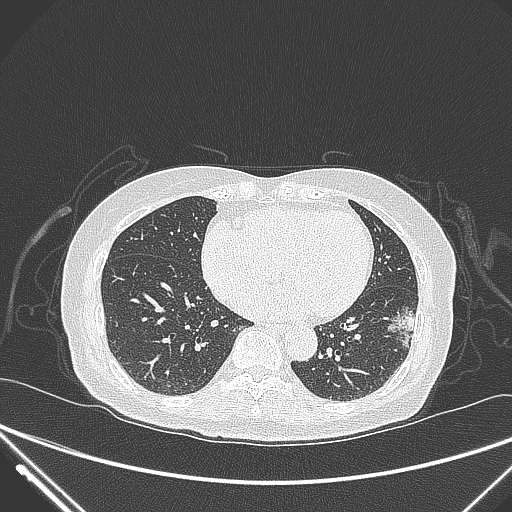
Chest CT, one axial slice; position 113 of 310 along the scan axis; lung window (W 1500 / L -600 HU); 1 mm slice thickness; 512 × 512 image matrix, field of view 377 × 377 mm. Female patient, age 82 years. Case-level facts recorded for this patient, not image findings: clinical TNM (as recorded): T1c N0 M0; histopathological grade: G2.
Annotated regions visible in this slice (bounding box drawn by a radiologist):
- lung tumour (recorded histology: adenocarcinoma): bounding box (x1, y1, x2, y2) in pixels: (381, 299, 421, 362)